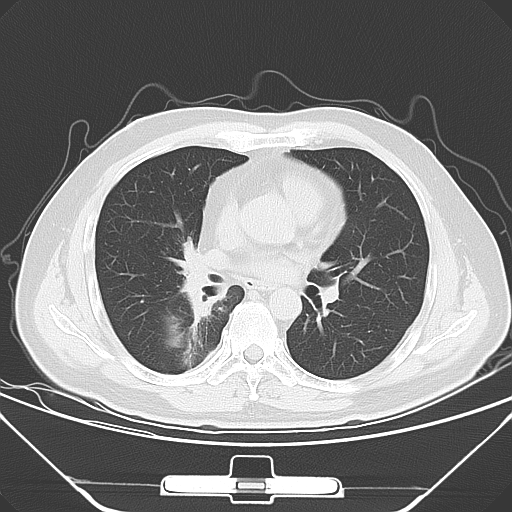
Chest CT, one axial slice. Slice 28 of 56 in the series (ordered by position). Lung window (W 1500 / L -600 HU). 512 × 512 image matrix, field of view 371 × 371 mm. Patient: male, 48 years. Case-level facts recorded for this patient, not image findings: clinical TNM (as recorded): T1a N1 M1c; histopathological grade: G3.
Structures marked on this image (bounding box drawn by a radiologist):
- lung tumour (recorded histology: adenocarcinoma): bounding box (x1, y1, x2, y2) in pixels: (175, 236, 211, 343)